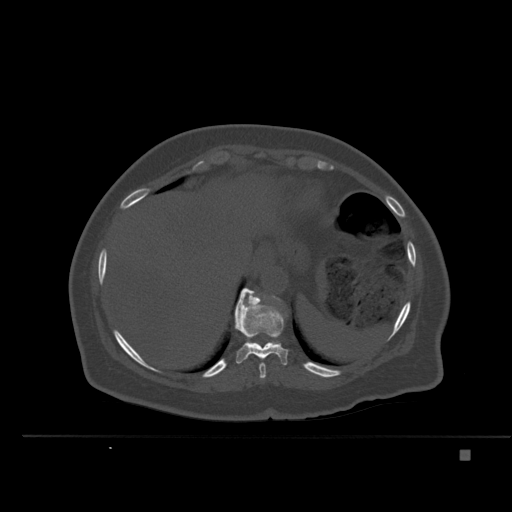
CT including the spine, one axial slice. Bone window (W 1800 / L 400 HU). 1.5 mm slice thickness. 512 × 512 image matrix. Patient: female, 74 years. Case-level facts recorded for this patient, not image findings: primary cancer: colon.
Outlined on this slice (semi-automatically segmented with operator editing):
- T10 vertebra: bounding box (x1, y1, x2, y2) in pixels: (235, 294, 289, 365)
- T11 vertebra: (236, 288, 279, 307)
- T9 vertebra: (259, 363, 266, 379)